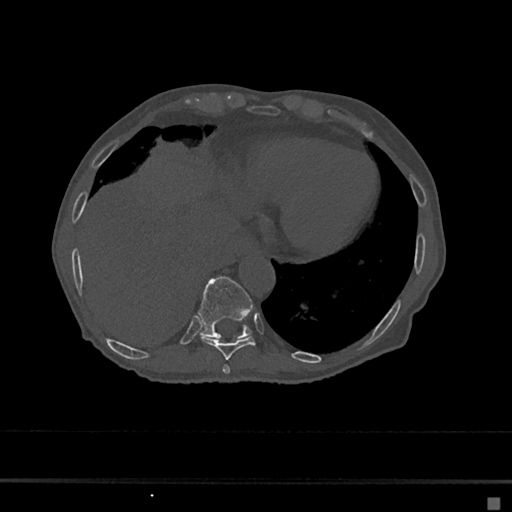
CT including the spine, one axial slice; slice 253 of 797 in the series (ordered by position); reconstruction kernel Br40s/3; 120 kVp; bone window (W 1800 / L 400 HU); 0.5 mm slice thickness; 512 × 512 image matrix, field of view 360 × 360 mm. Female patient, age 68 years. From the clinical record (not read from this slice): primary cancer: renal.
Outlined on this slice (semi-automatically segmented with operator editing):
- T10 vertebra: box from (x=198, y=276) to (x=253, y=339) px
- T8 vertebra: (x=222, y=365)–(x=231, y=375)
- T9 vertebra: (x=200, y=336)–(x=256, y=360)